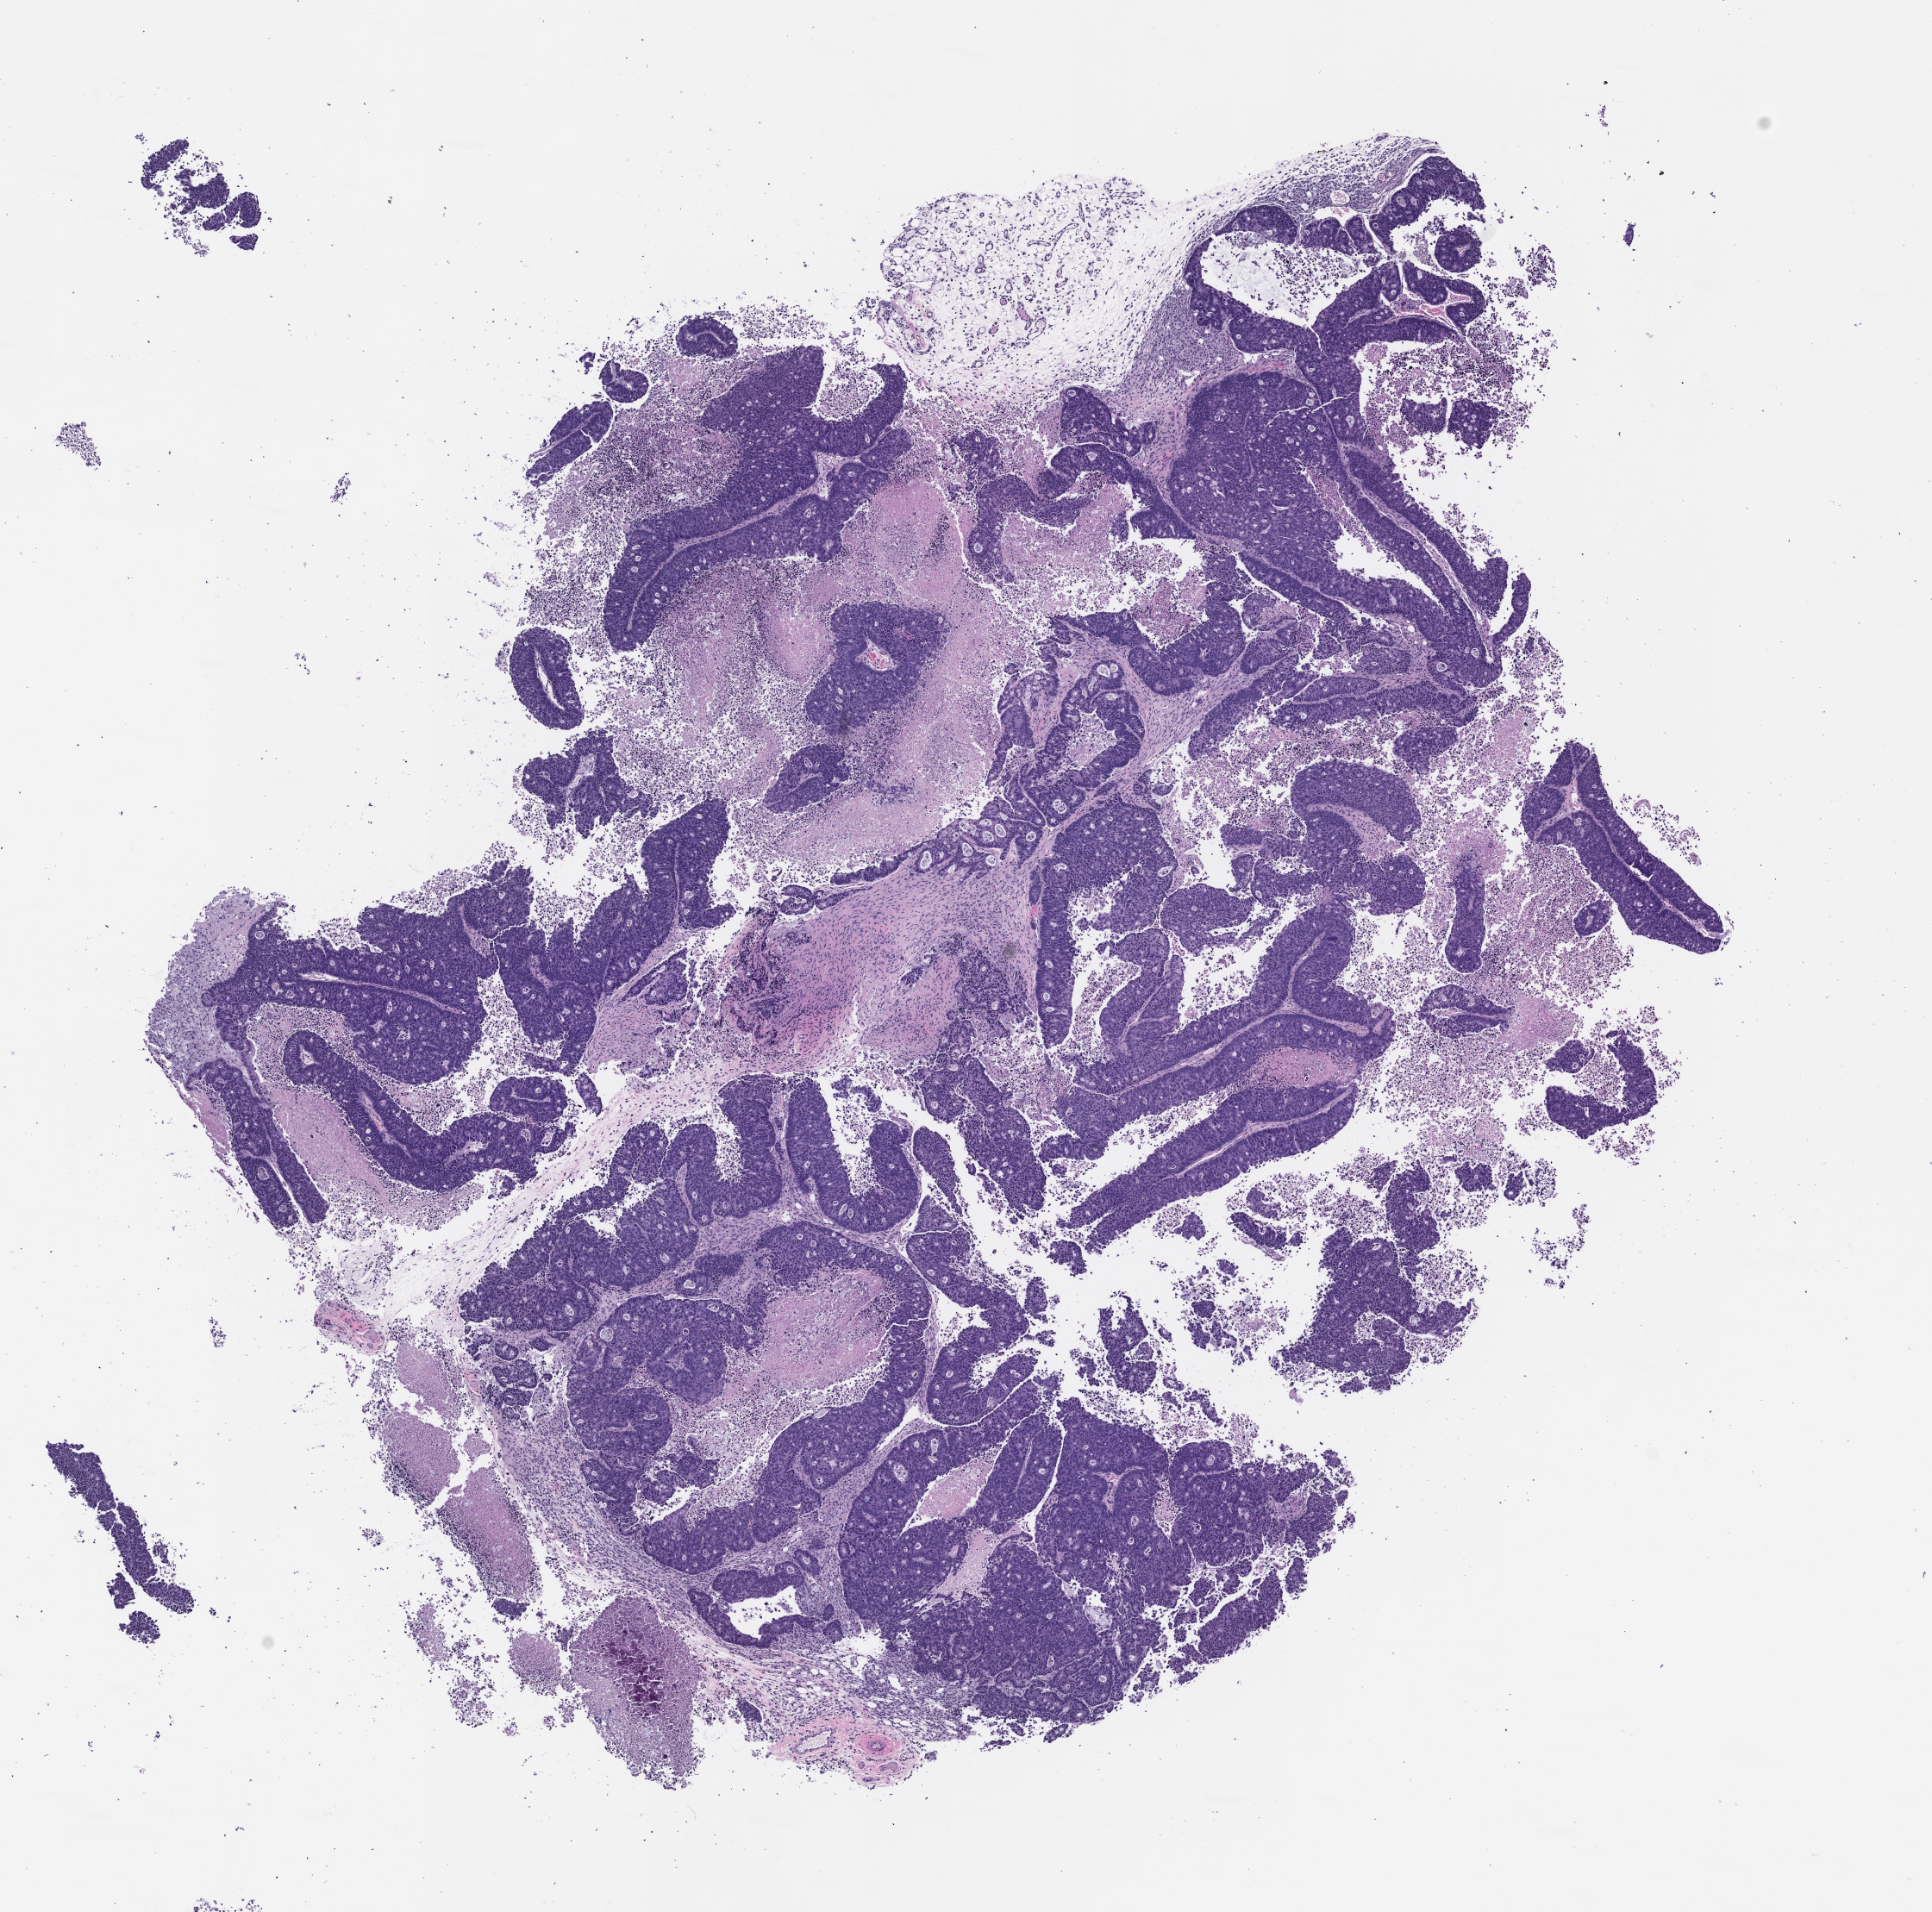
Whole-slide image, hematoxylin and eosin (H&E): patient-derived xenograft (human tumor grown in a mouse), passage 0, shown as a low-resolution overview of the whole scanned area (about 9.0 x 8.9 mm), formalin-fixed paraffin-embedded section, originating tumor site category: rectum.
Originating patient diagnosis: Rectal Adenocarcinoma.